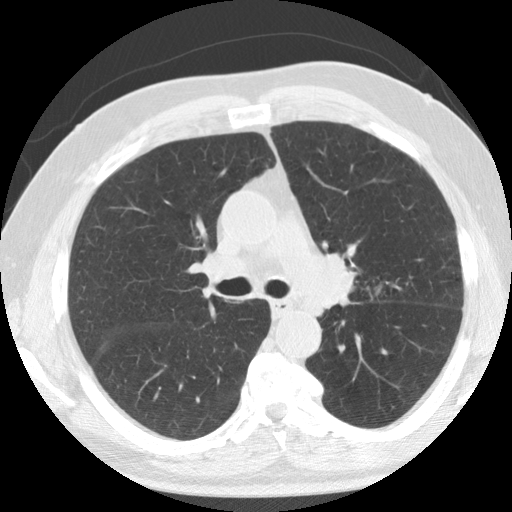
Axial slice from a low-dose chest CT screening exam. Second screening round (one year after baseline). Lung window (W 1500 / L -600 HU). 2.5 mm slice thickness. Standard (soft-tissue) reconstruction kernel (STANDARD). Male participant, aged 74 years at enrolment.
• Expert-annotated lung lesion, bounding box (x1, y1, x2, y2) in pixels: (300, 239, 367, 309).
• No non-calcified nodule or mass ≥4 mm was recorded by the screening reader at this exam.
• Official screen result: positive, other.
• Participant outcome: lung cancer diagnosed 274 days after this screen — non-small cell carcinoma, left upper lobe, poorly differentiated (G3), stage IIB (AJCC 6th edition).